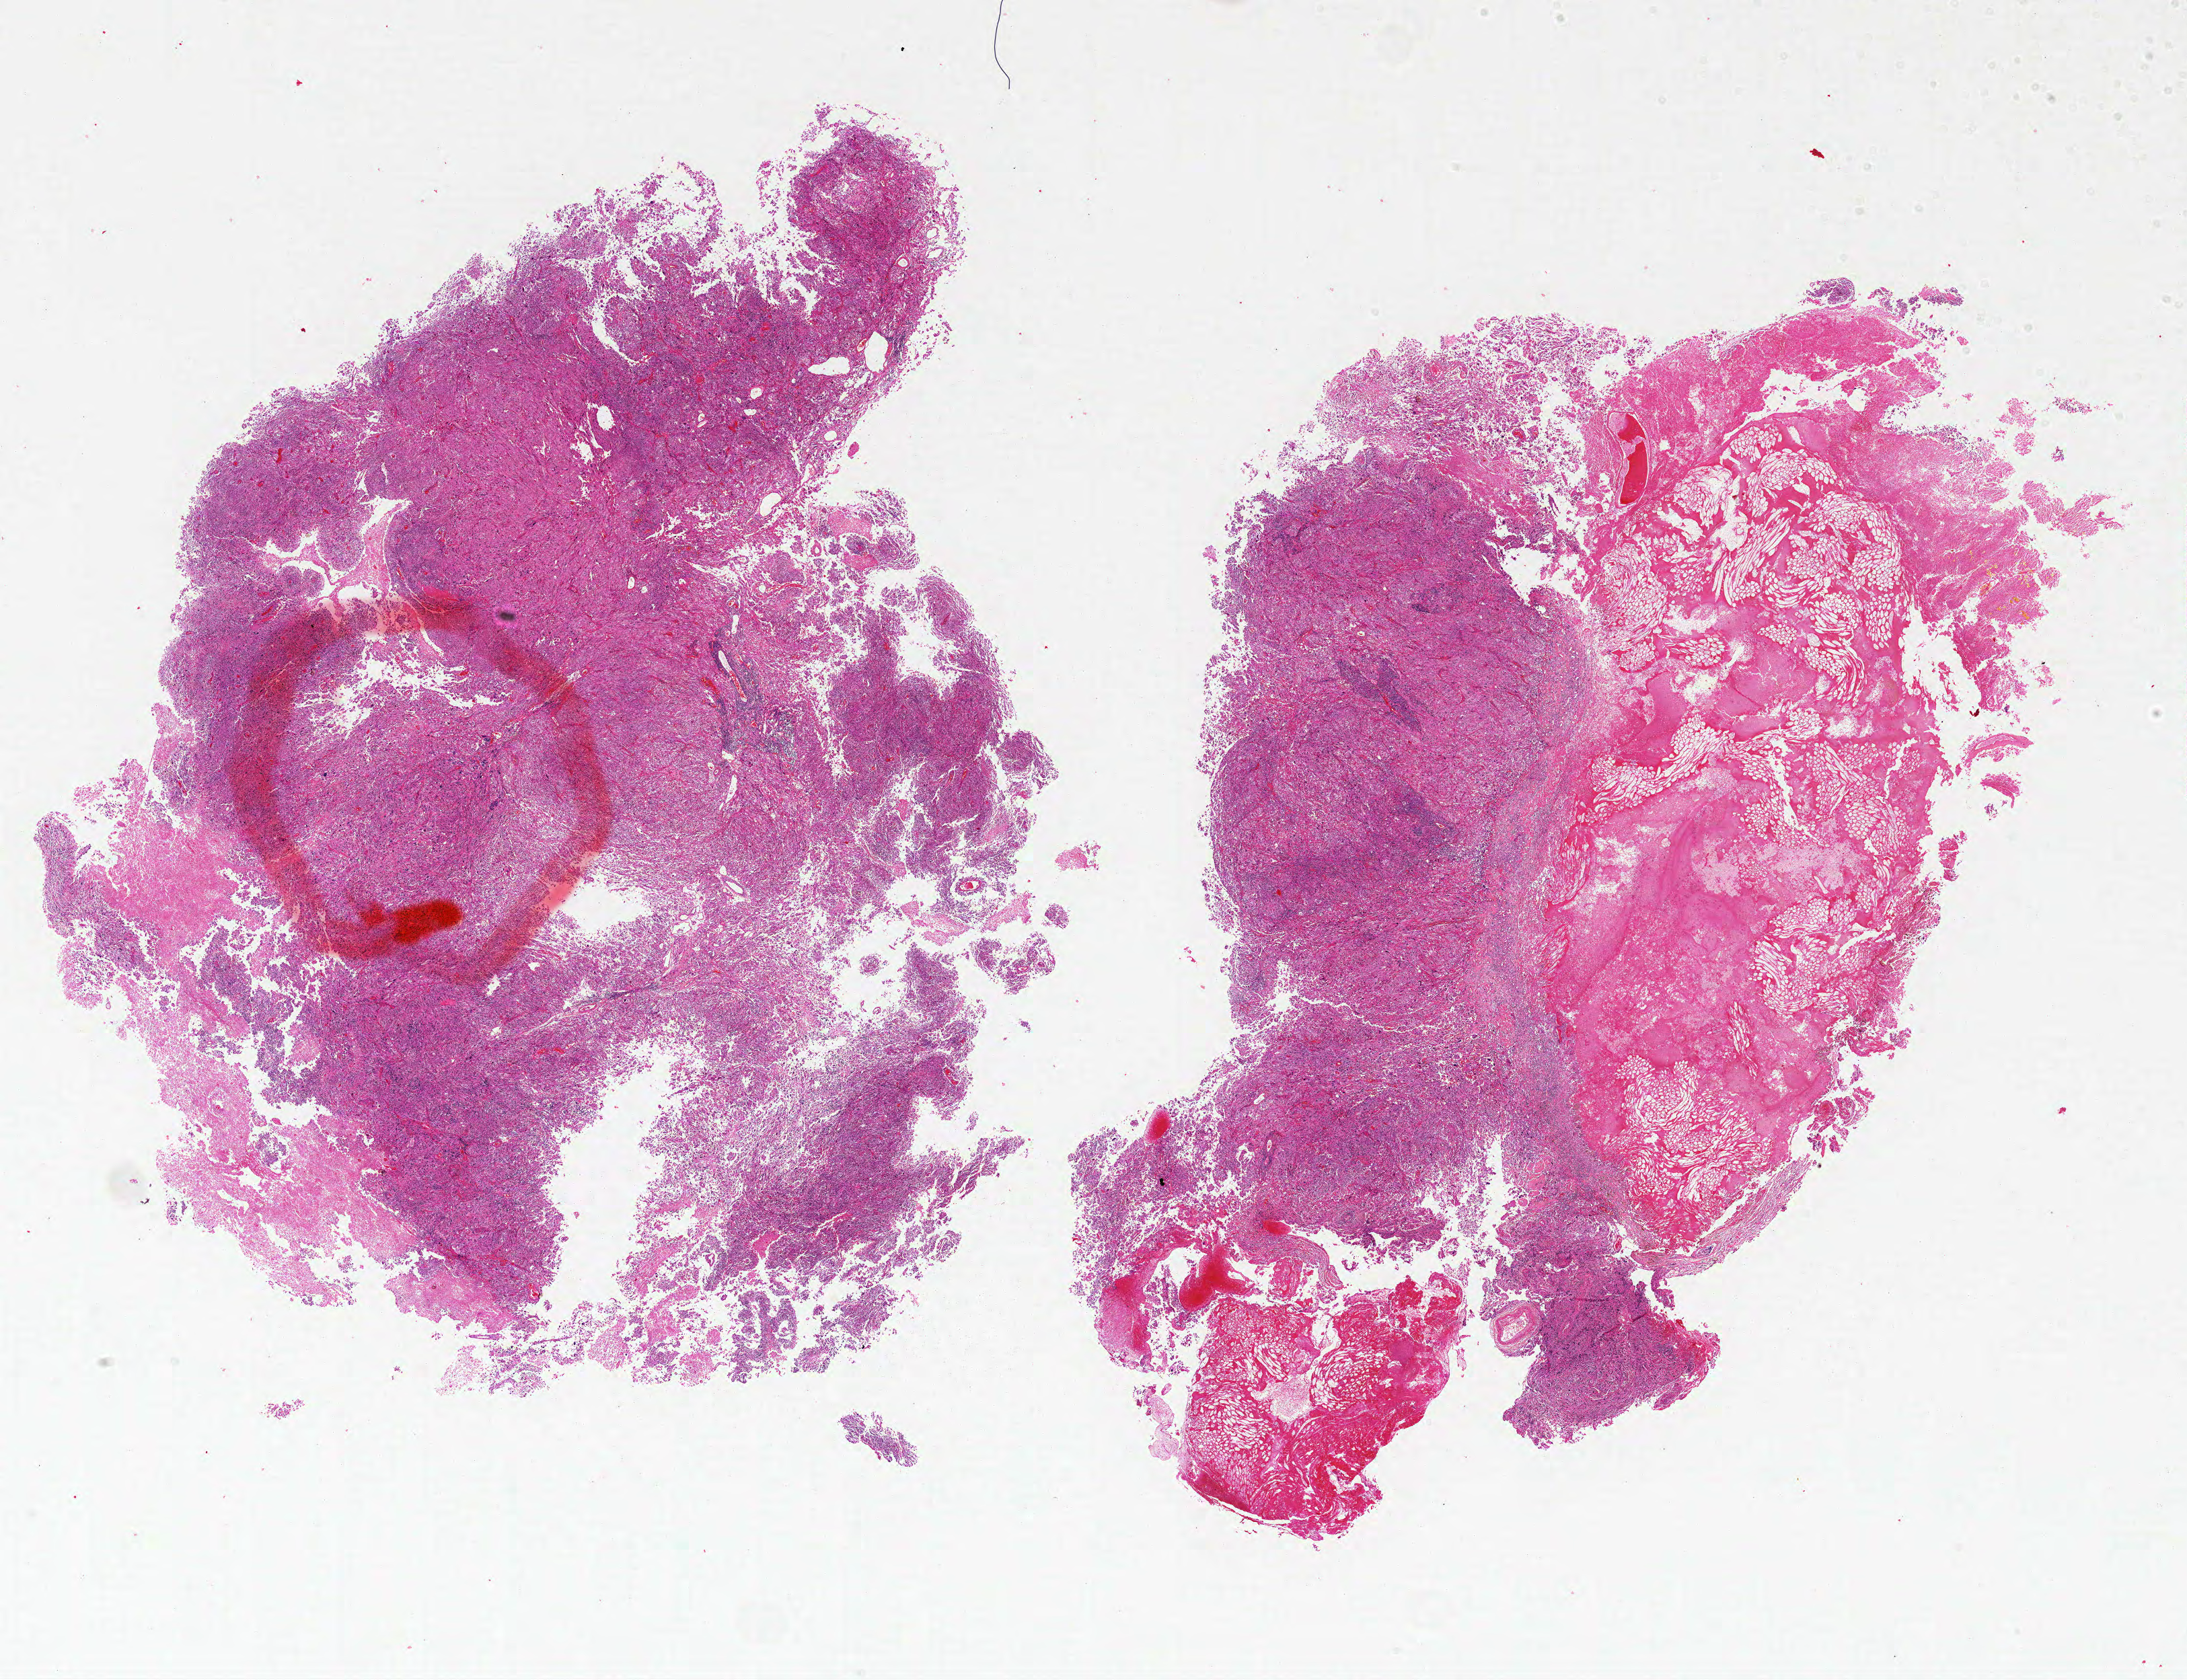
Whole-slide histology image, Hematoxylin and eosin (H&E) stained — shown as a low-resolution overview of the whole scanned area (about 26.0 x 20.0 mm, acquisition: 20x scan); formalin-fixed paraffin-embedded (FFPE) diagnostic section; primary tumour sample from the brain. Male patient; age at initial diagnosis 58 years.
- pathologic diagnosis: Glioblastoma